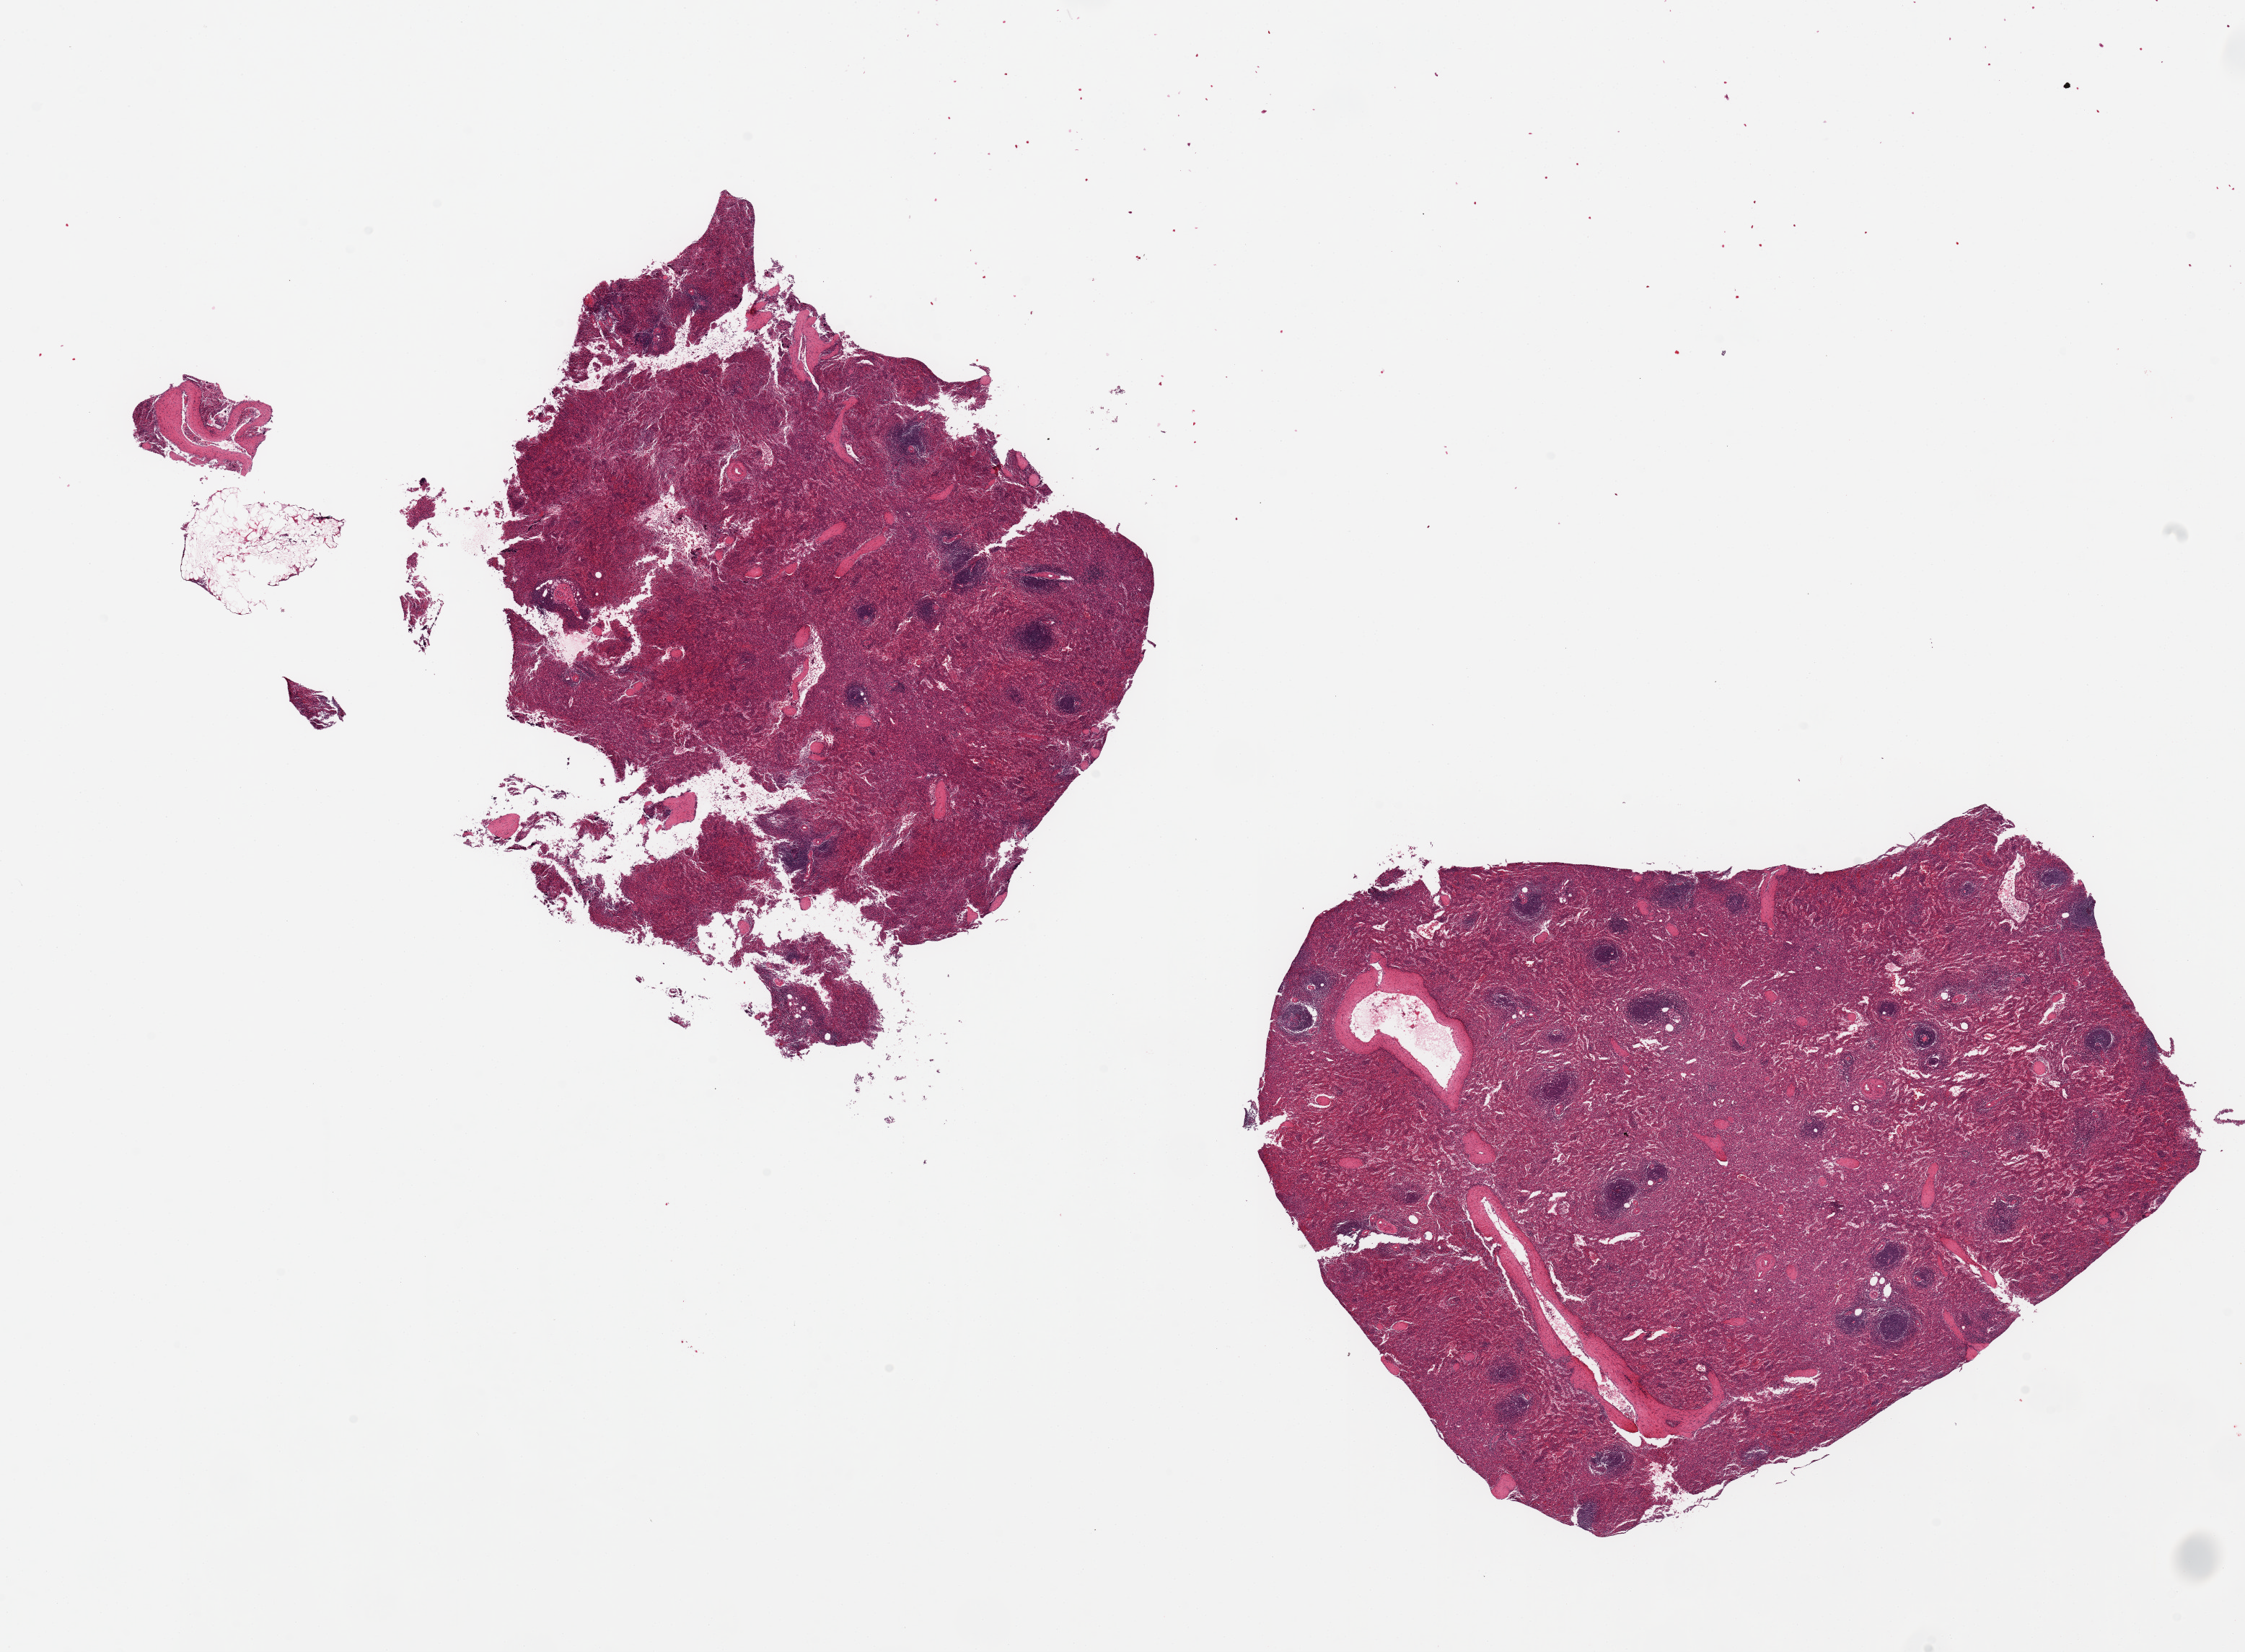
Whole-slide image, haematoxylin and eosin stain, brightfield — whole scanned area (about 24.6 x 18.1 mm) shown as a low-resolution overview, PAXgene-fixed, paraffin-embedded tissue, target tissue: spleen, donor tissue sample.
Review note (as recorded): 2 pieces 9x8 & 7x6 mm; focally congested.